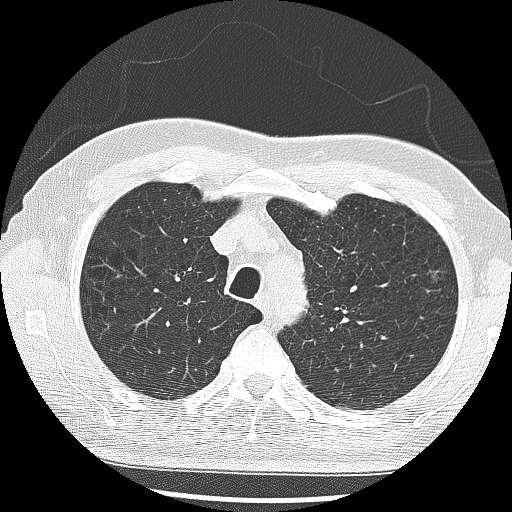
Low-dose screening chest CT, one axial slice; slice 219 of 285 in the series (ordered by position); lung window (W 1500 / L -600 HU); 2.5 mm slice thickness; 512 × 512 image matrix, field of view 340 × 340 mm.
Annotated regions visible in this slice (outlined manually by an expert reader):
- lesion 1 (tumor, upper lobe of left lung): box from (x=430, y=273) to (x=441, y=284) px